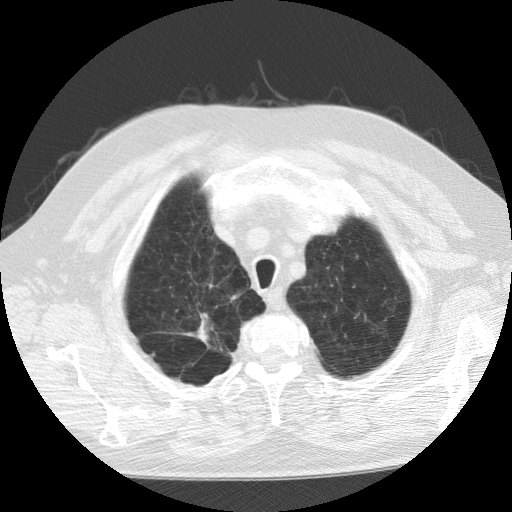
Chest CT (low-dose screening protocol), one axial image; second screening round (one year after baseline); lung window (W 1500 / L -600 HU); standard (soft-tissue) reconstruction kernel (STANDARD); slice 15 of 109 in the series. Male participant, aged 64 years at enrolment. Current smoker at enrolment.
• Expert-annotated lung lesion, bounding box <181,311,230,360> (left, top, right, bottom; pixels).
• The screening reader recorded 2 non-calcified nodules or masses ≥4 mm on this exam; which of them this box marks is not recorded.
• Lung cancer was diagnosed 233 days after this screen: squamous cell carcinoma, NOS, left upper lobe, moderately differentiated (G2), stage IA (AJCC 6th edition), 10 mm at pathology.